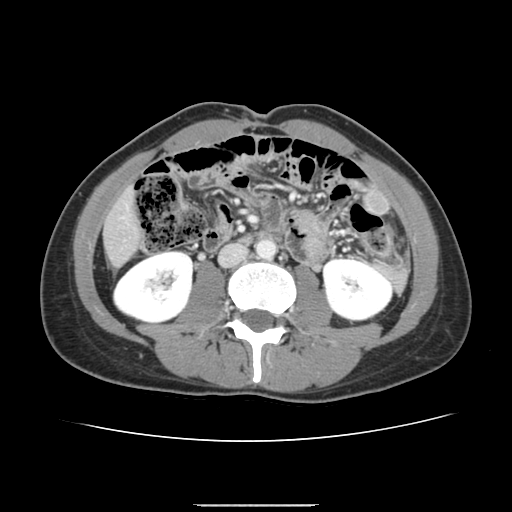
Contrast-enhanced abdominal CT, one axial slice; position 40 of 150 along the scan axis; 120 kVp; soft-tissue window (W 400 / L 40 HU); 2.5 mm slice thickness; 512 × 512 image matrix, field of view 324 × 324 mm. Female patient, age 32 years. From the clinical record (not read from this slice): diagnosis: colorectal cancer liver metastases, imaged before liver resection; multiple liver metastases: yes; largest metastasis: 0.7 cm; disease in both lobes: no.
Outlined on this slice (expert manual segmentation):
- liver: bounding box (x1, y1, x2, y2) in pixels: (105, 193, 140, 265)
- planned liver remnant (the part of the liver to remain after resection): (105, 193, 140, 265)